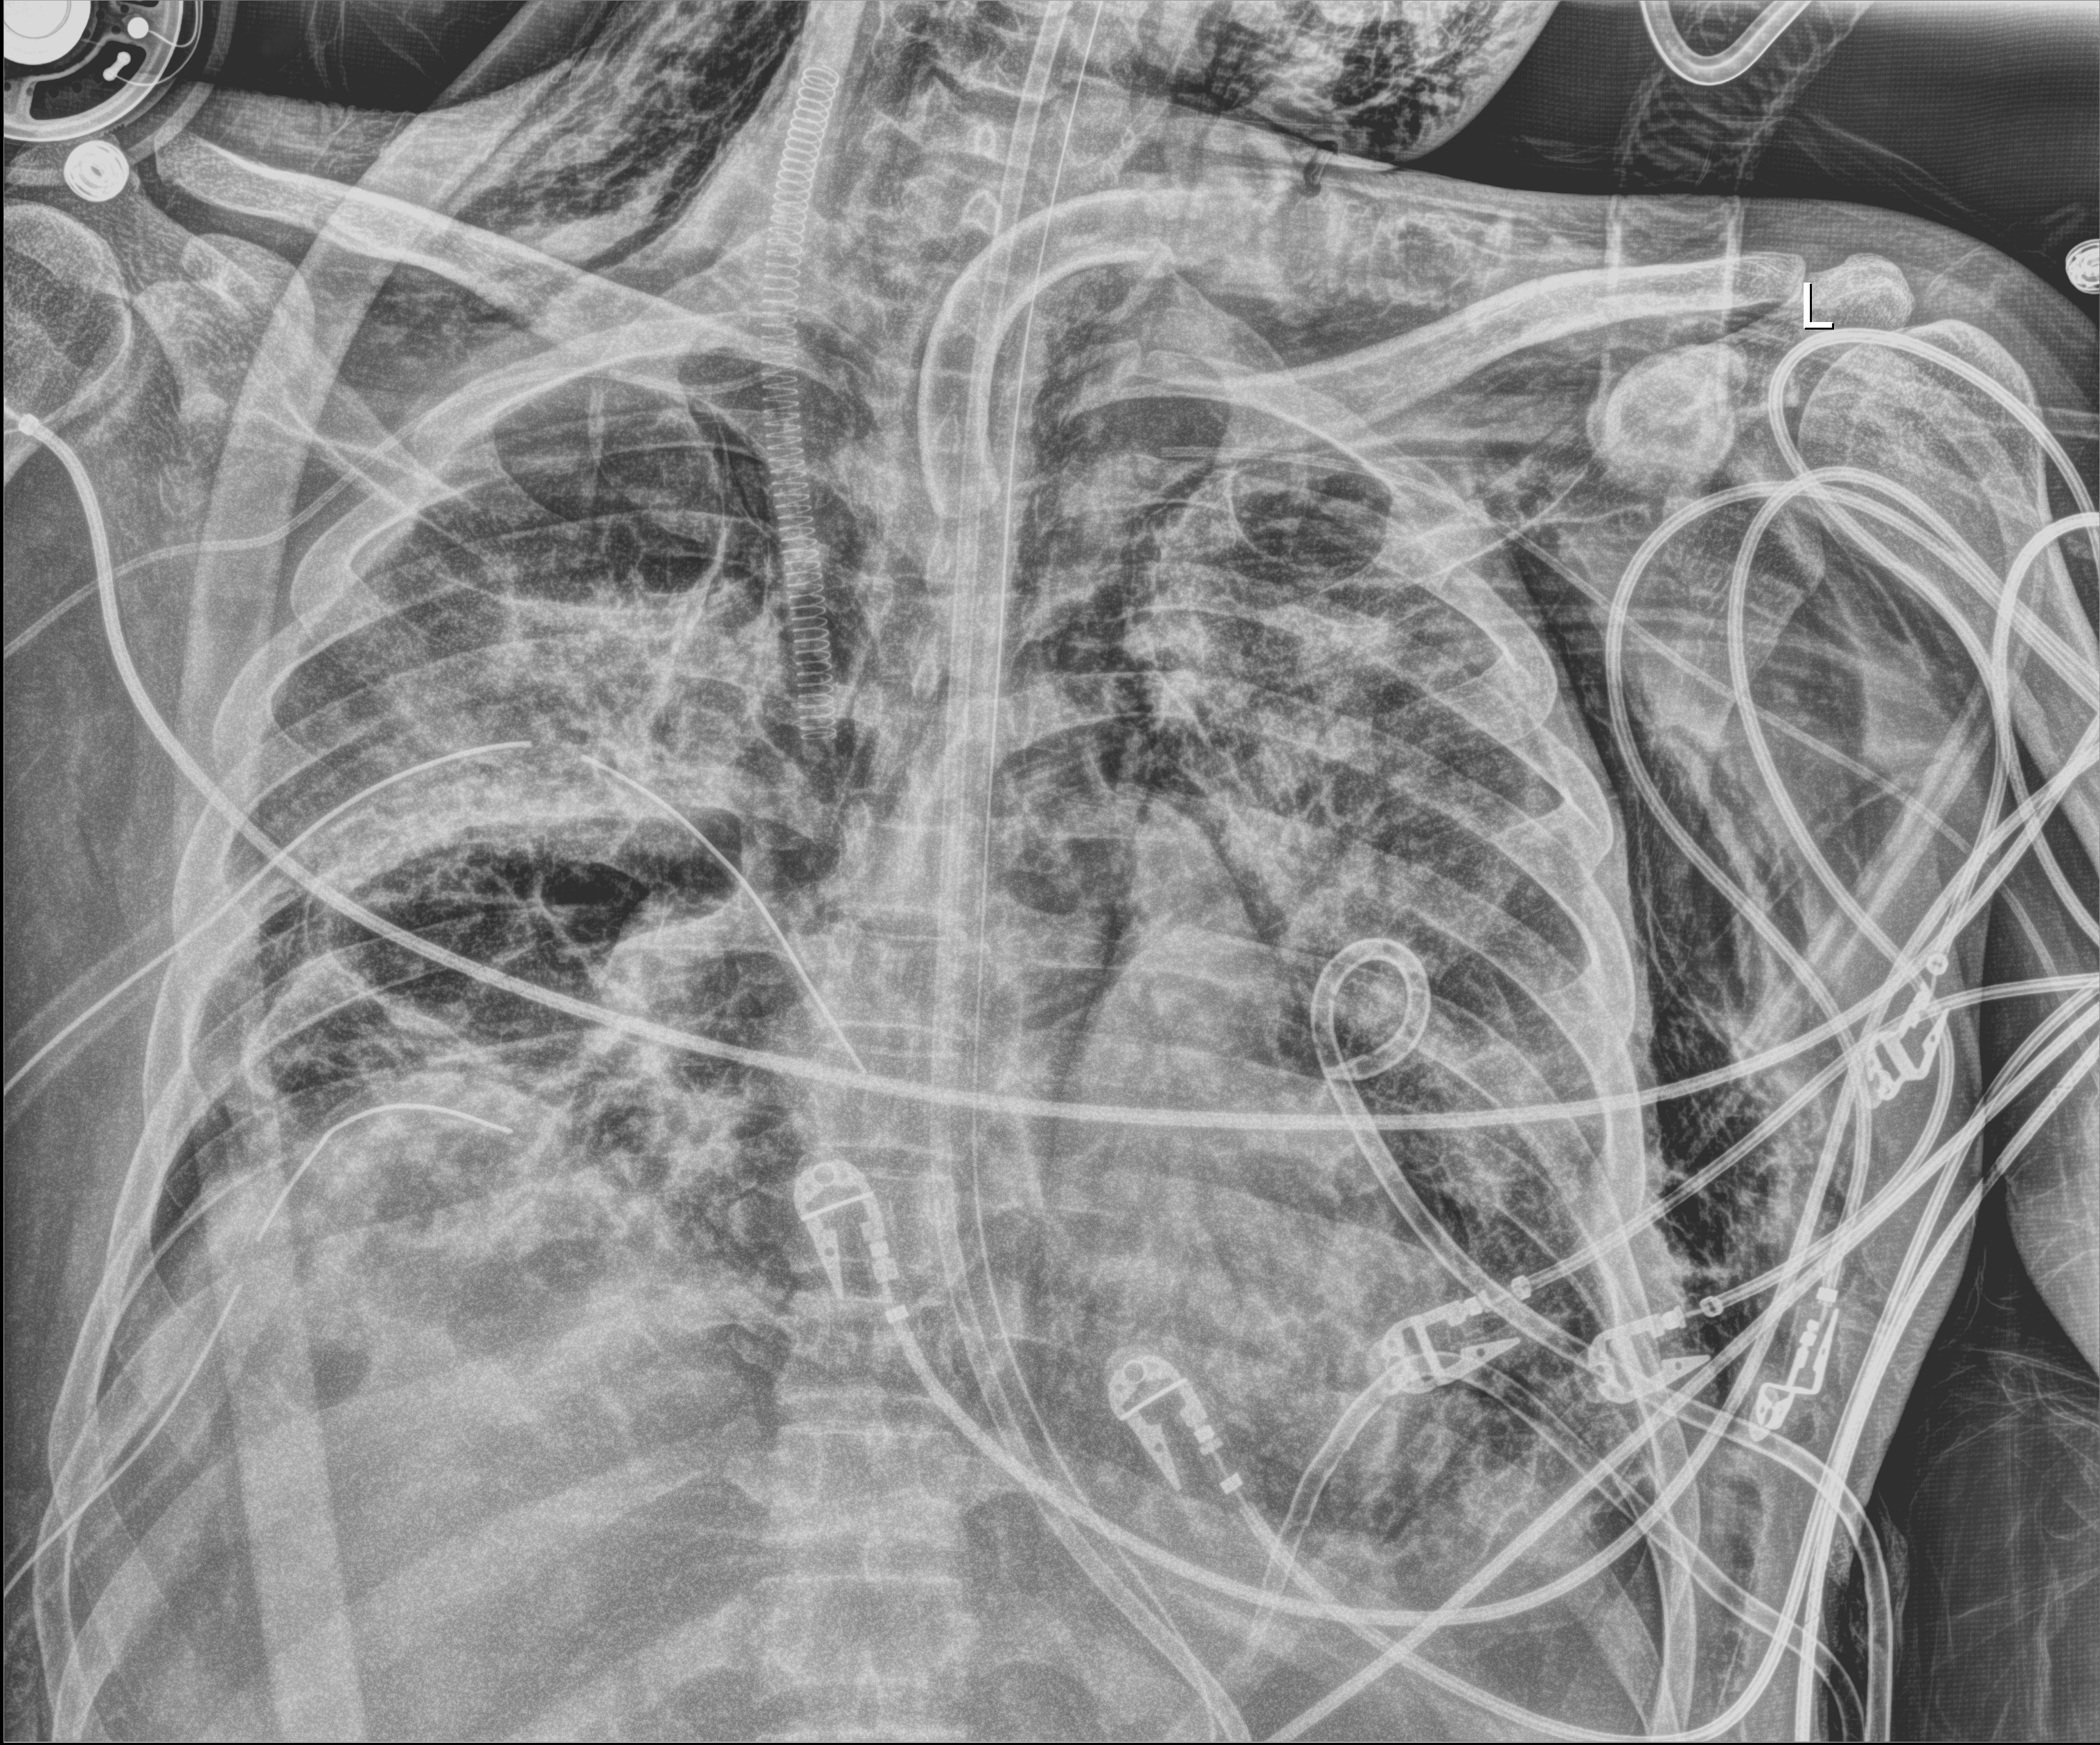
Chest X-ray (portable); anteroposterior (AP) projection. Adult patient hospitalised with COVID-19, age 18–59 years.
From the hospital-stay record, not from the radiograph (when in the stay this image was taken is not recorded):
- COPD (admission record): no
- smoking status (admission record): never
- hypertension (admission record): no